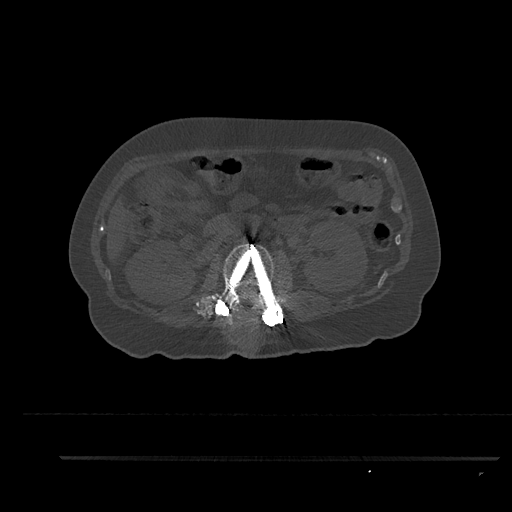
CT including the spine, one axial slice; position 173 of 797 along the scan axis; bone window (W 1800 / L 400 HU); 0.5 mm slice thickness; 512 × 512 image matrix. Female patient, age 44 years. Case-level facts recorded for this patient, not image findings: primary cancer: renal.
Structures marked on this image (semi-automatically segmented with operator editing):
- L2 vertebra: bounding box [x1, y1, x2, y2] px = [213, 243, 276, 320]